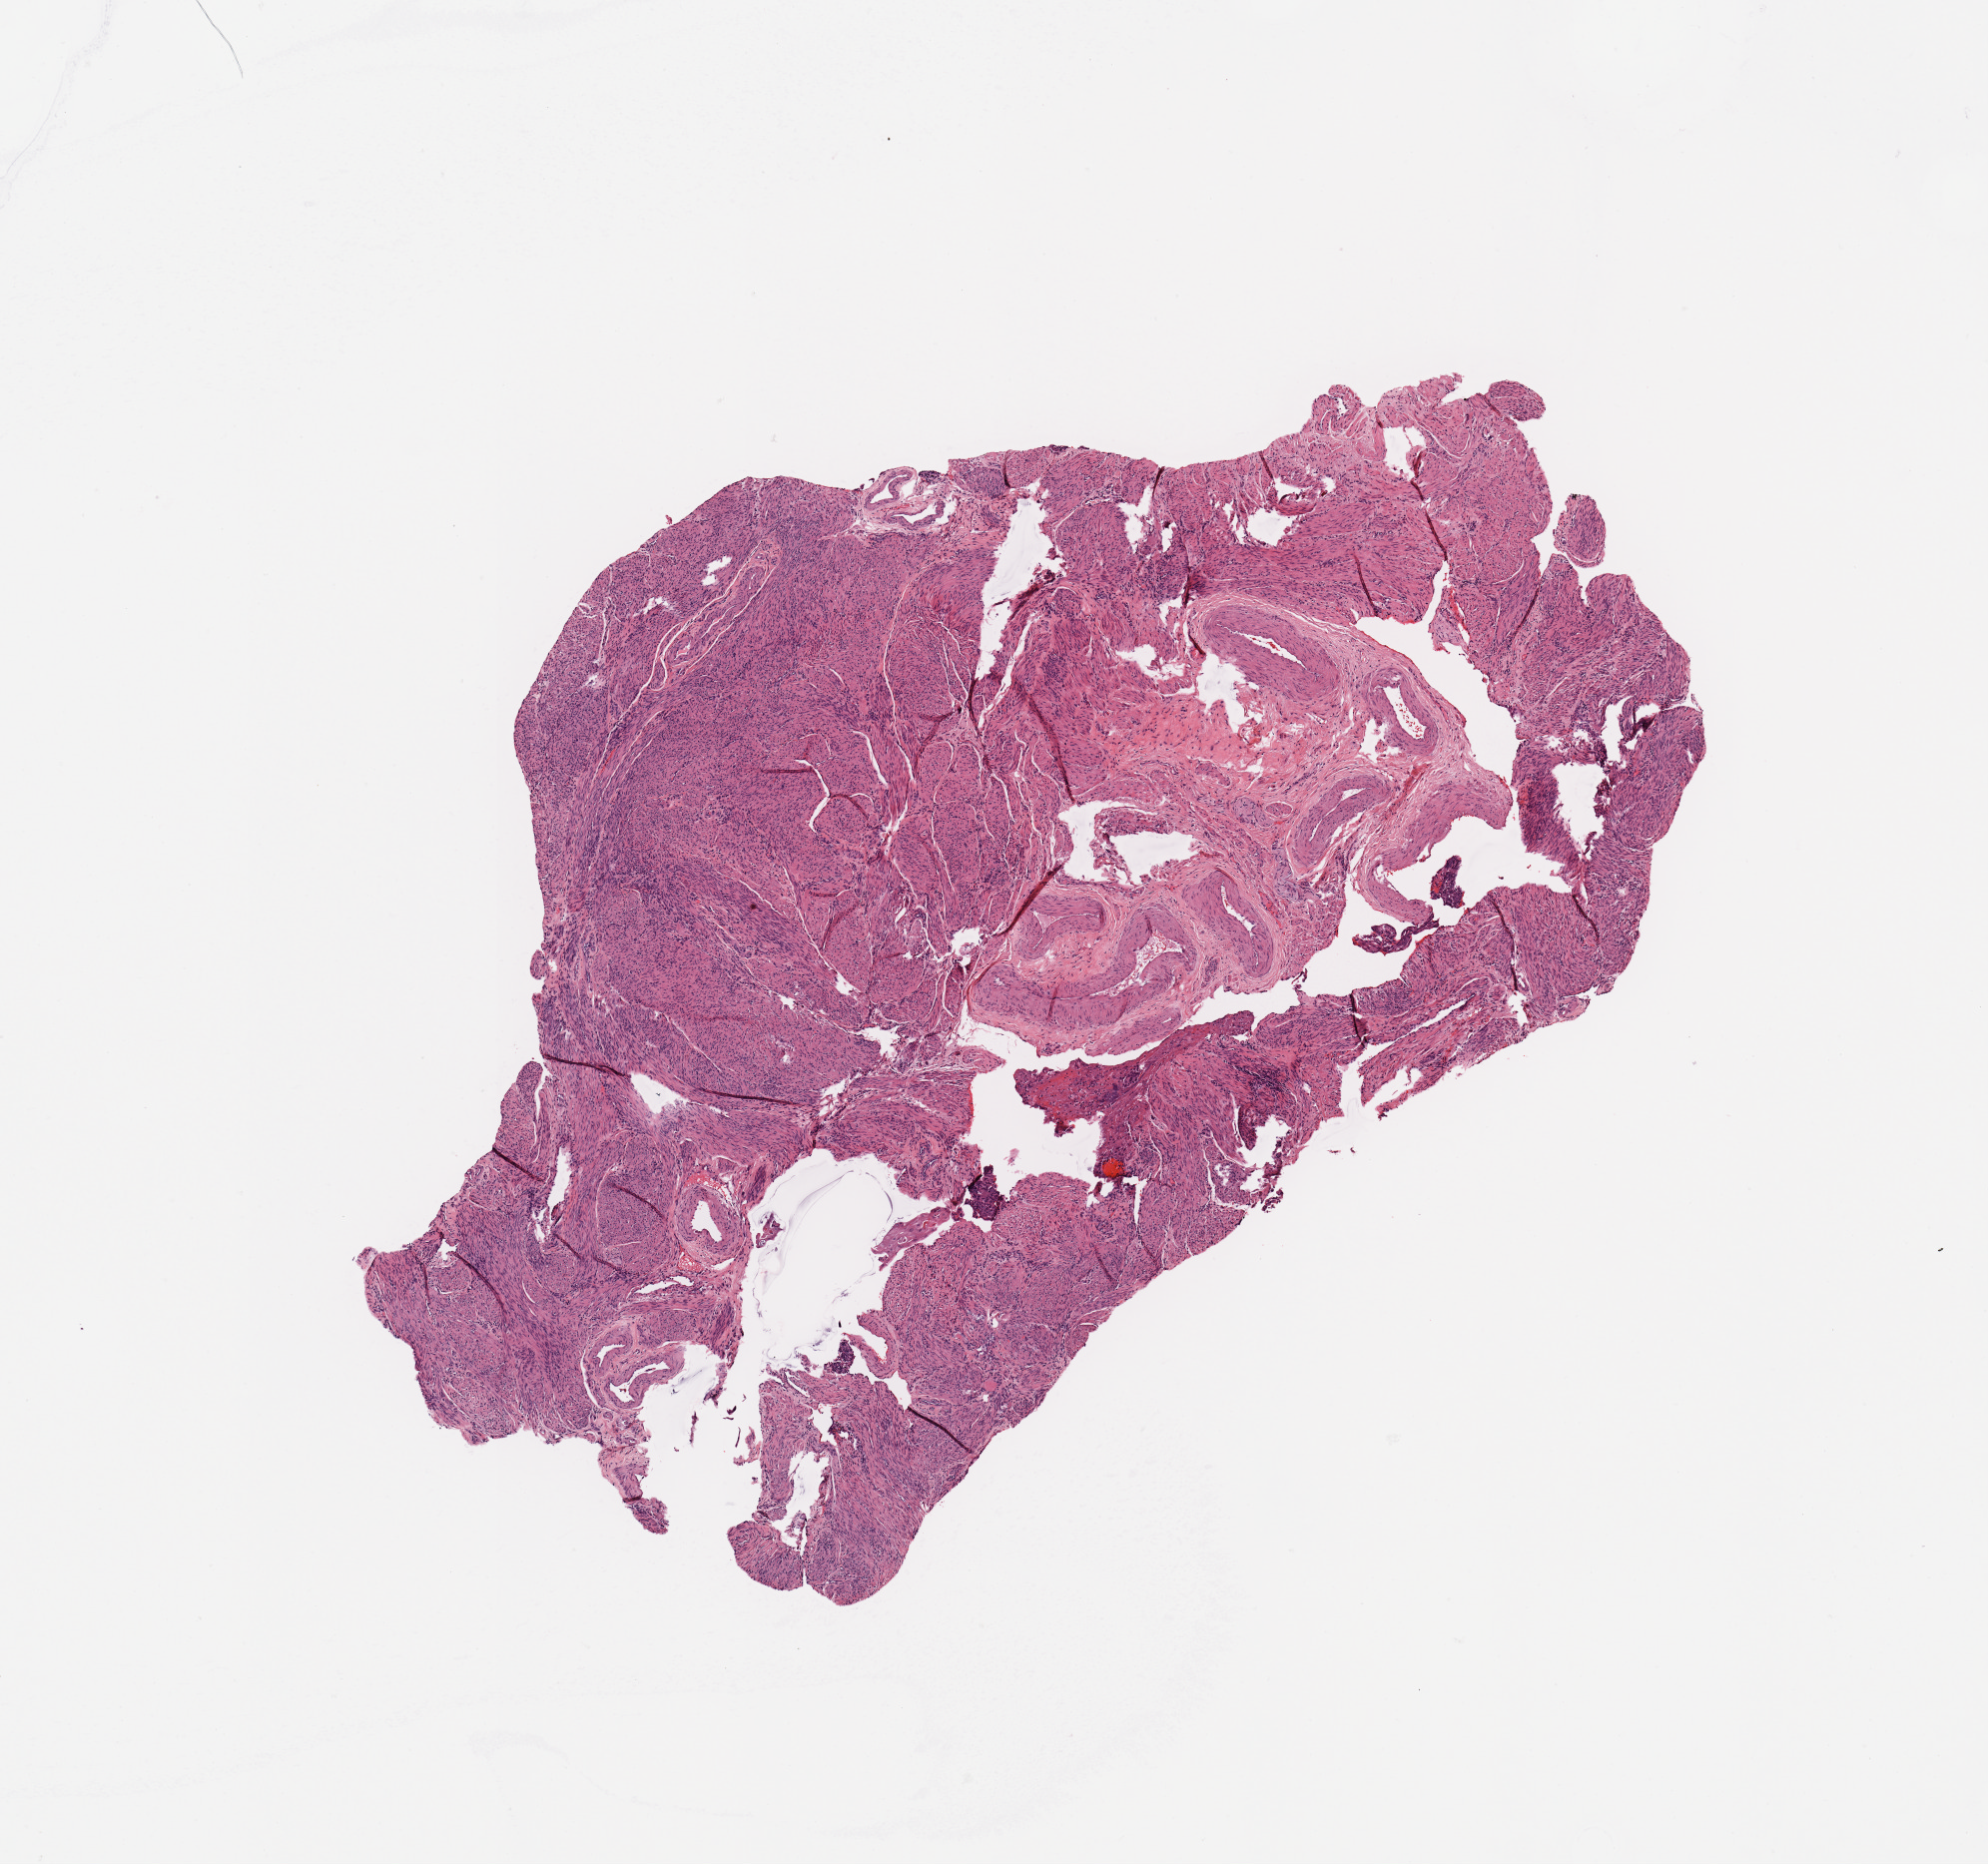
Hematoxylin and eosin (H&E) stained whole-slide image — whole scanned area (about 7.9 x 7.4 mm, slide scanned at 20x) shown as a low-resolution overview; normal (non-tumour) tissue sample, uterus. Female, 54 y/o.
This section: normal (non-tumour) tissue from the same patient. Patient diagnosis: Endometrioid adenocarcinoma, NOS.